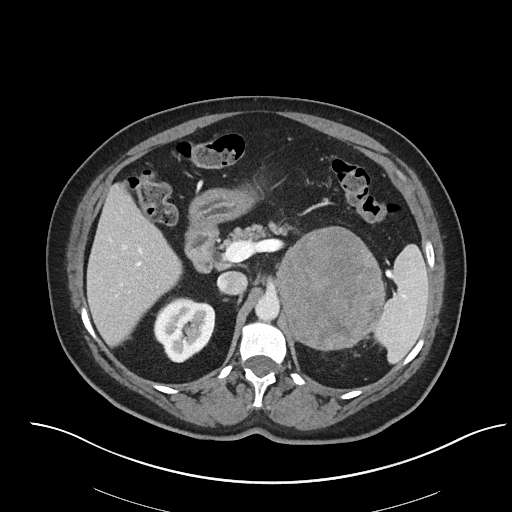
Contrast-enhanced abdominal CT, one axial slice; position 48 of 92 along the scan axis; reconstruction kernel I40f/2; 120 kVp; intravenous contrast given; soft-tissue window (W 400 / L 40 HU); 3 mm slice thickness; 512 × 512 image matrix. Patient: female, 53 years. From the clinical record (not read from this slice): diagnosis: adrenocortical carcinoma; tumour side: left adrenal; tumour size at pathology: 9 cm; Ki-67 index: 28 %; stage (as recorded): 2.
Annotated regions visible in this slice (semi-automatic segmentation, software-assisted and operator-edited):
- mass: bounding box [x1, y1, x2, y2] px = [278, 228, 384, 349]